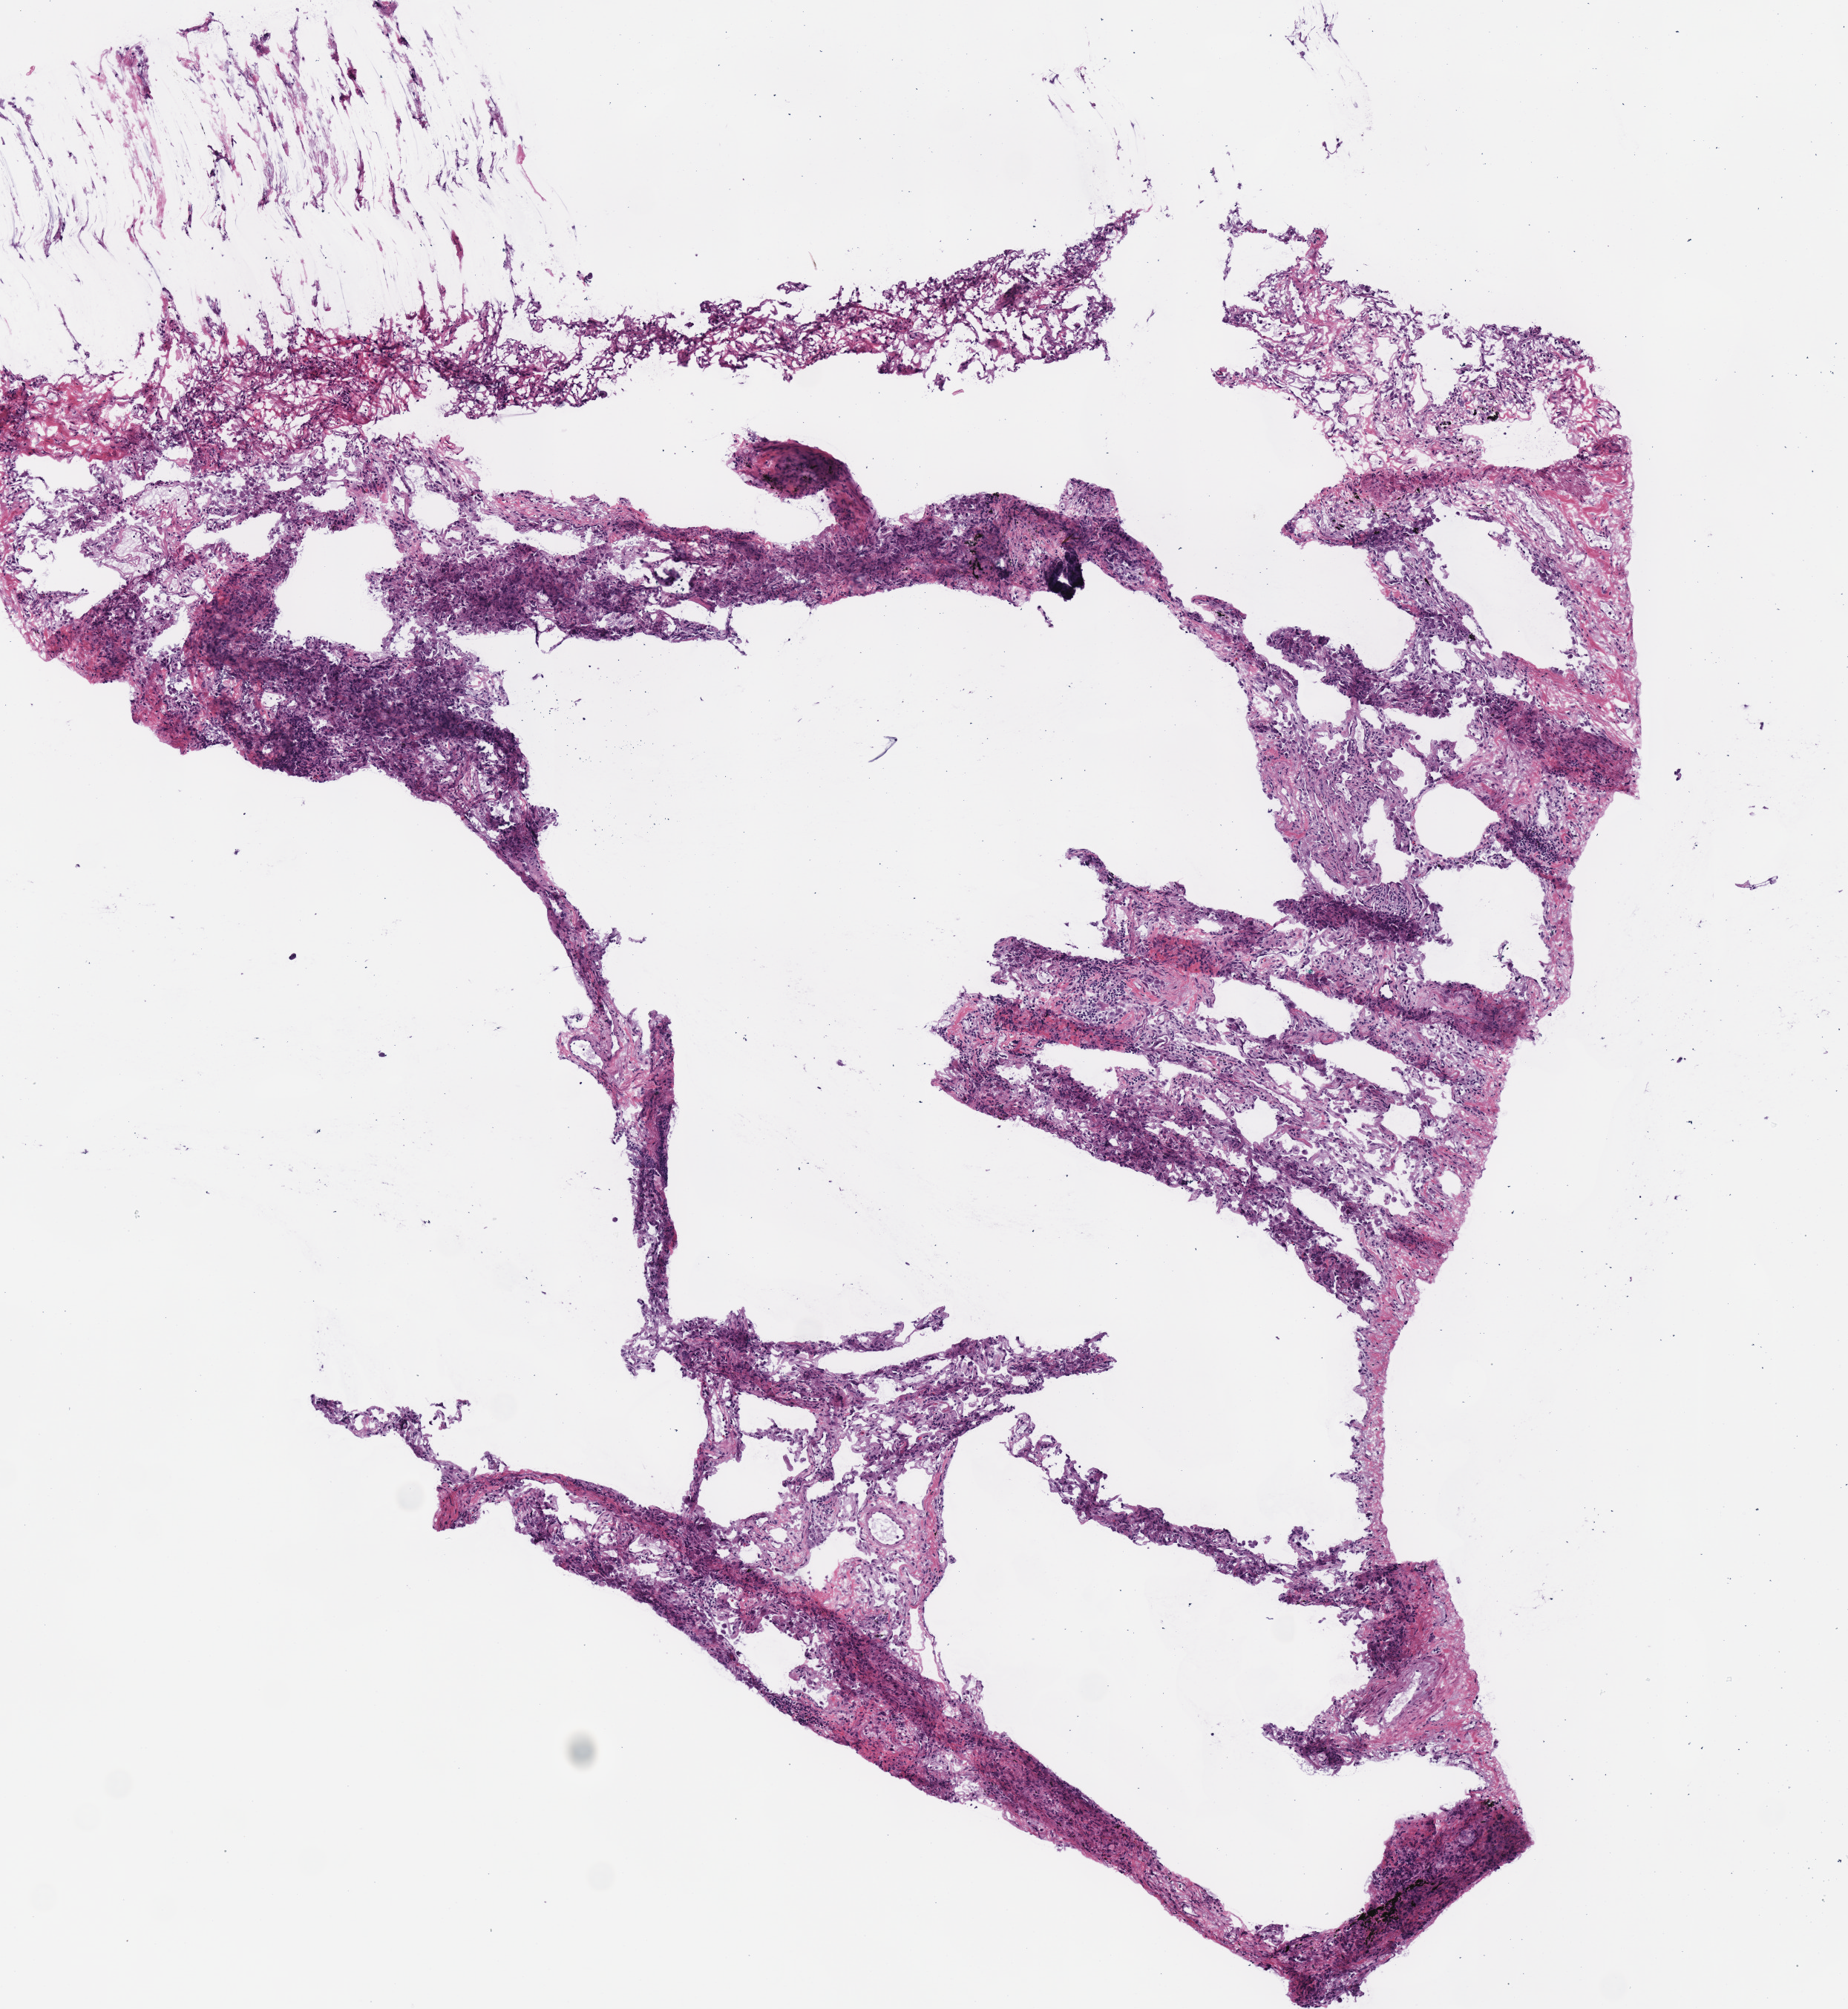
H&E-stained whole-slide image, a low-resolution overview of the entire scanned area, about 4.9 x 5.3 mm (slide scanned at 40x), frozen section from the top of the tissue portion, sample: solid tissue normal (non-tumour tissue), lung. Male, age 70 years at initial diagnosis.
This section: solid tissue normal (non-tumour) sample from the same patient. Patient diagnosis: Squamous cell carcinoma, NOS (upper lobe, lung).